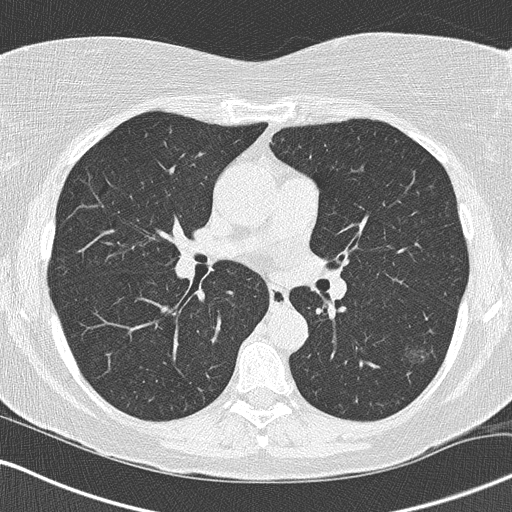
Low-dose screening chest CT, one axial slice; slice 83 of 160 in the series (ordered by position); reconstruction kernel B50f; 120 kVp; lung window (W 1500 / L -600 HU); 2 mm slice thickness; 512 × 512 image matrix, field of view 327 × 327 mm.
Structures marked on this image (outlined manually by an expert reader):
- lesion 1 (tumor, lower lobe of left lung): bounding box <404,348,430,363> (left, top, right, bottom; pixels)